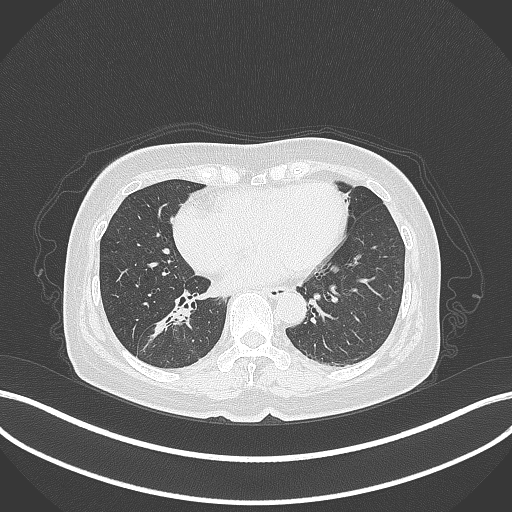
Chest CT, one axial slice; slice 155 of 429 in the series (ordered by position); reconstruction kernel B70f; 120 kVp; lung window (W 1500 / L -600 HU); 1 mm slice thickness; 512 × 512 image matrix, field of view 400 × 400 mm. Patient: female, 67 years. Case-level facts recorded for this patient, not image findings: clinical TNM (as recorded): T1c N1 M0.
Outlined on this slice (bounding box drawn by a radiologist):
- lung tumour (recorded histology: adenocarcinoma): bounding box <140,301,198,354> (left, top, right, bottom; pixels)